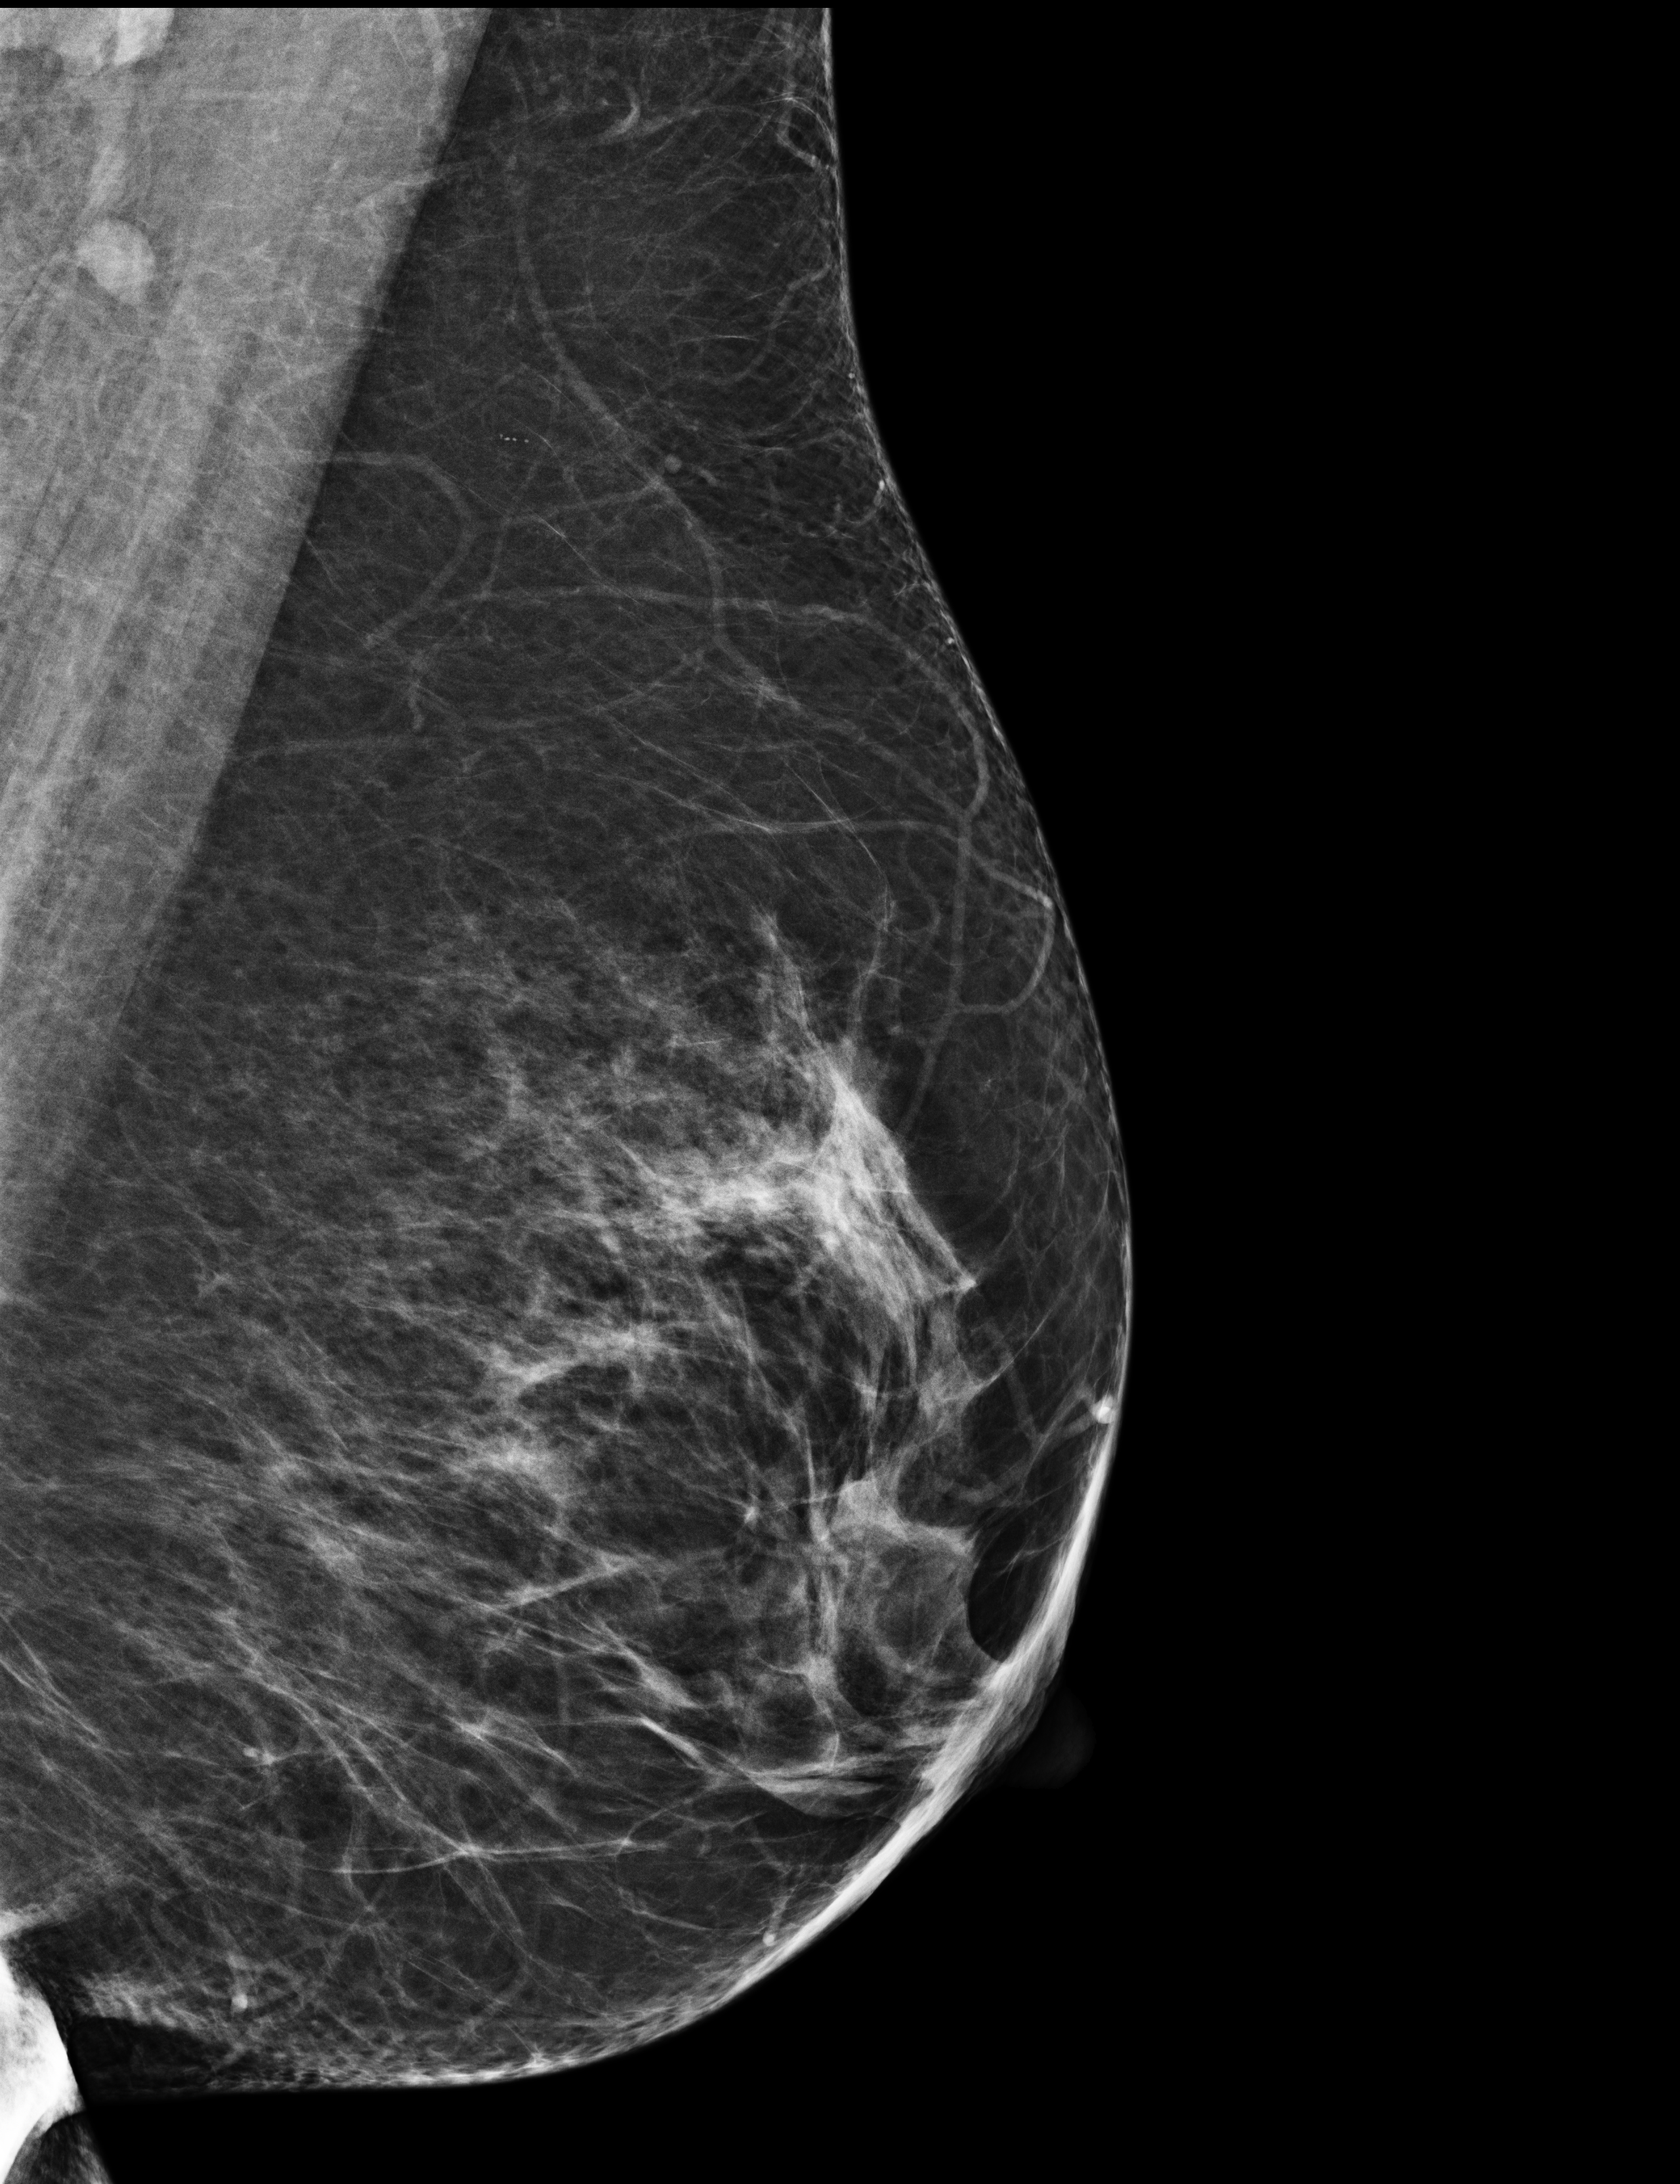
Screening examination. Patient: female, 57 years.
Image type: full-field digital mammogram. Breast: left. Projection: MLO view.